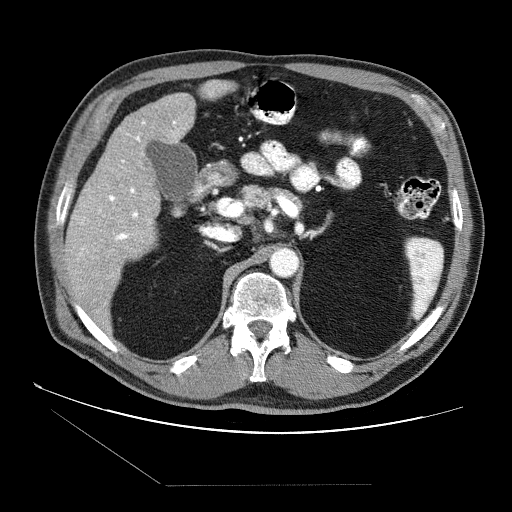
Contrast-enhanced abdominal CT (liver protocol), one axial slice. Slice 38 of 87 in the series (ordered by position). Soft-tissue window (W 400 / L 40 HU). 2.5 mm slice thickness. 512 × 512 image matrix, field of view 400 × 400 mm. From the clinical record (not read from this slice): diagnosis: hepatocellular carcinoma (patient treated with transarterial chemoembolisation; whether this scan precedes or follows treatment is not stated here); TNM stage (as recorded): Stage-II; Child-Pugh class: B; tumour nodularity: multinodular; tumour size: 2.6 cm.
Annotated regions visible in this slice (semi-automatically segmented with operator editing):
- liver parenchyma outside the tumour (the mass and vessels are separate outlines, so this box may not span the whole liver): box from (x=64, y=80) to (x=236, y=324) px
- liver vessels: (x=76, y=121)–(x=178, y=310)